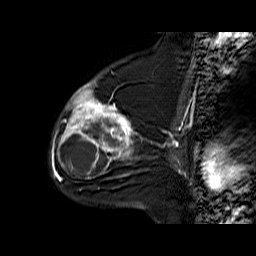
Breast MRI (dynamic contrast-enhanced), one sagittal slice. Position 41 of 60 along the scan axis. Dynamic contrast-enhanced series, time point 2 of 6 at this slice position (early post-contrast). 1.5 T. TE 6.3 ms, TR 32.9 ms. 4 mm slice thickness. 256 × 256 image matrix, field of view 200 × 200 mm. Female patient. From the clinical record (not read from this slice): setting: breast cancer imaged before/during neoadjuvant chemotherapy; receptor status: triple-negative.
Annotated regions visible in this slice (semi-automatically segmented with operator editing):
- analysis volume of interest (the breast-tissue region the enhancement analysis was run in; not a lesion): bounding box <57,76,139,170> (left, top, right, bottom; pixels)
- tumour enhancement mask (voxels above the 100 % enhancement threshold inside the analysis volume of interest): <59,83,132,168>